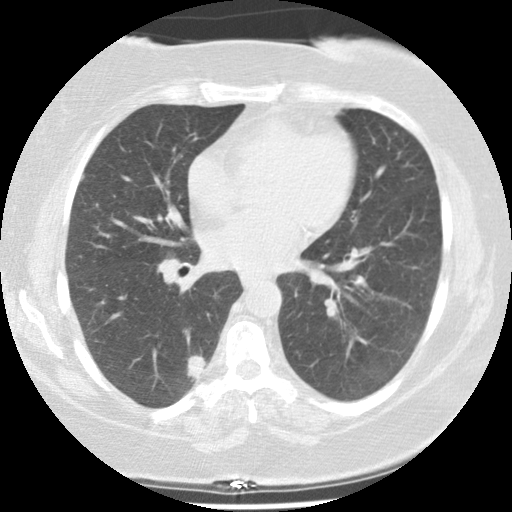
Chest CT (low-dose screening protocol), one axial image; second annual screen; lung window (W 1500 / L -600 HU); 2.5 mm slice thickness; slice 58 of 131 in the series; 512 × 512 image matrix, field of view 320 × 320 mm. Female, age 58 years at enrolment. Current smoker at enrolment.
Expert-annotated lung lesion, box from (x=163, y=334) to (x=220, y=399) px. The screening reader recorded 4 non-calcified nodules or masses ≥4 mm on this exam; which of them this box marks is not recorded. Official screen result: positive, other. Participant outcome: lung cancer diagnosed 299 days after this screen — adenocarcinoma, NOS, right lower lobe, stage IIIA (AJCC 6th edition), 25 mm at pathology.